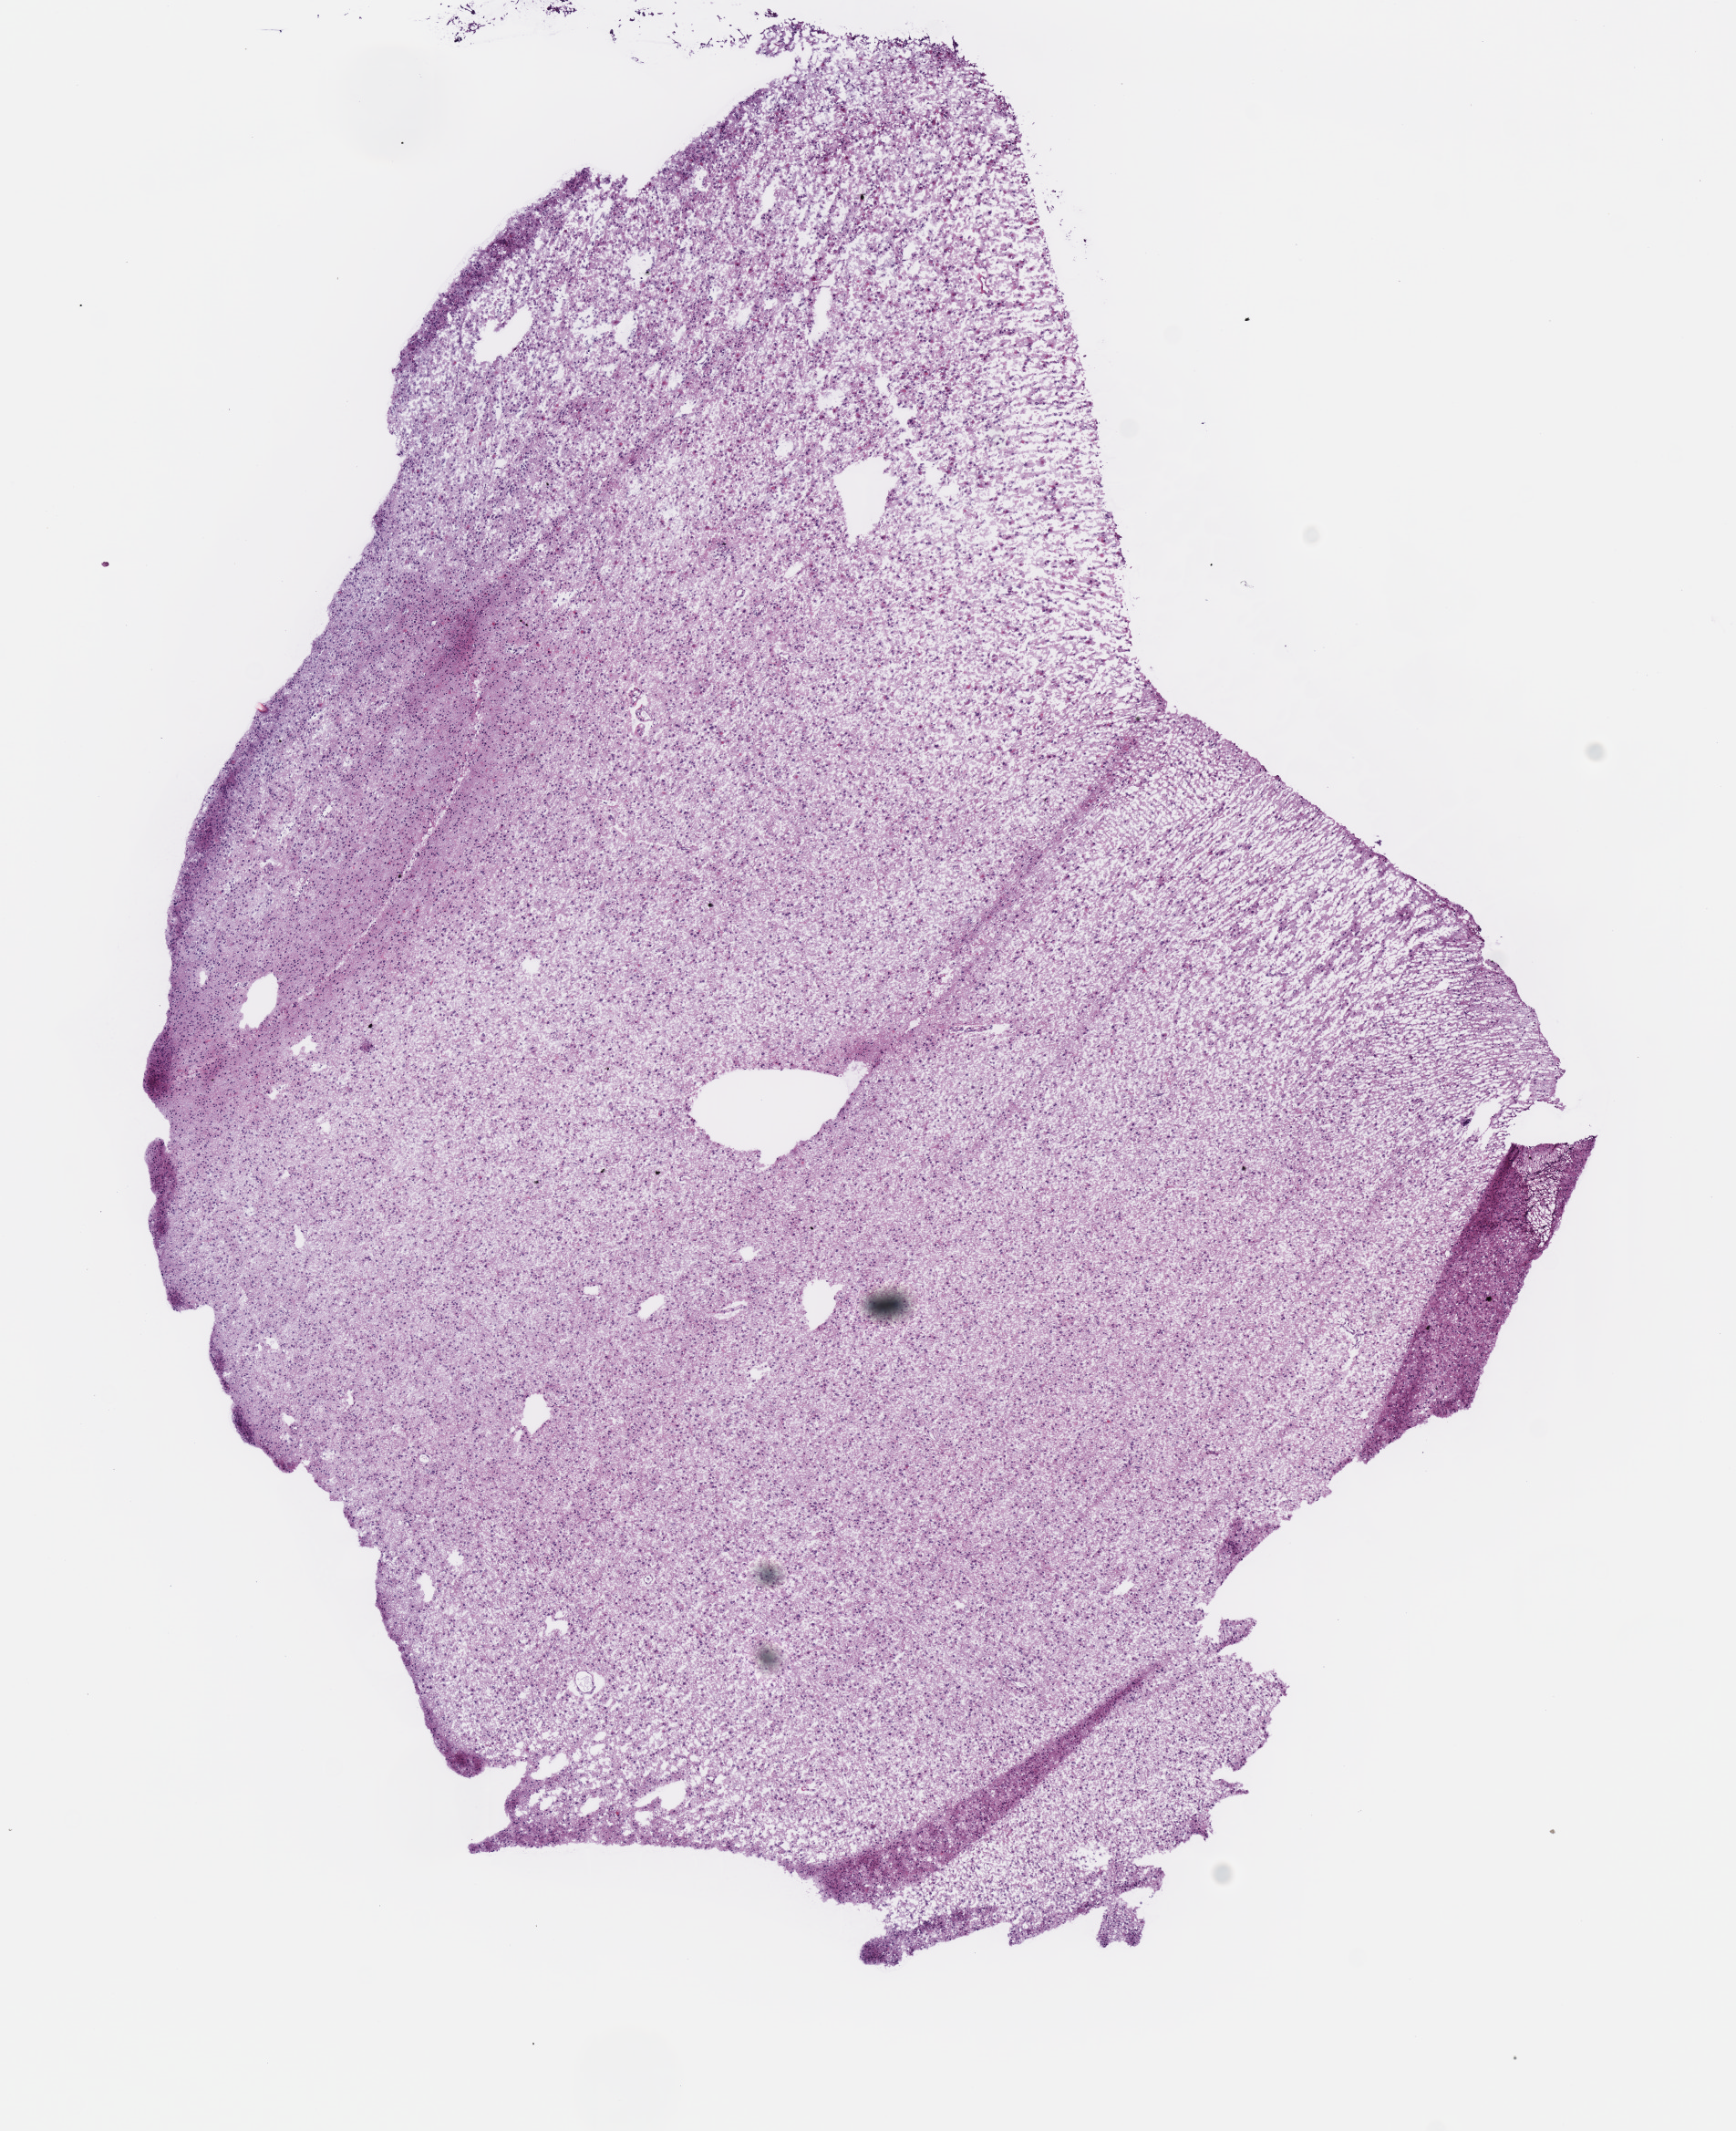
Whole-slide histology image, H&E-stained, whole scanned area (about 7.5 x 9.2 mm) shown as a low-resolution overview; frozen section from the top of the tissue portion; brain, primary tumour sample. Male, age 36 years at initial diagnosis. Histologic grade: G2 (moderately differentiated). Slide review estimates, as recorded: tumour cells 100%, tumour nuclei 75%, normal cells 0%, stromal cells 0%, necrosis 0%.
Histologic diagnosis: Mixed glioma (cerebrum).